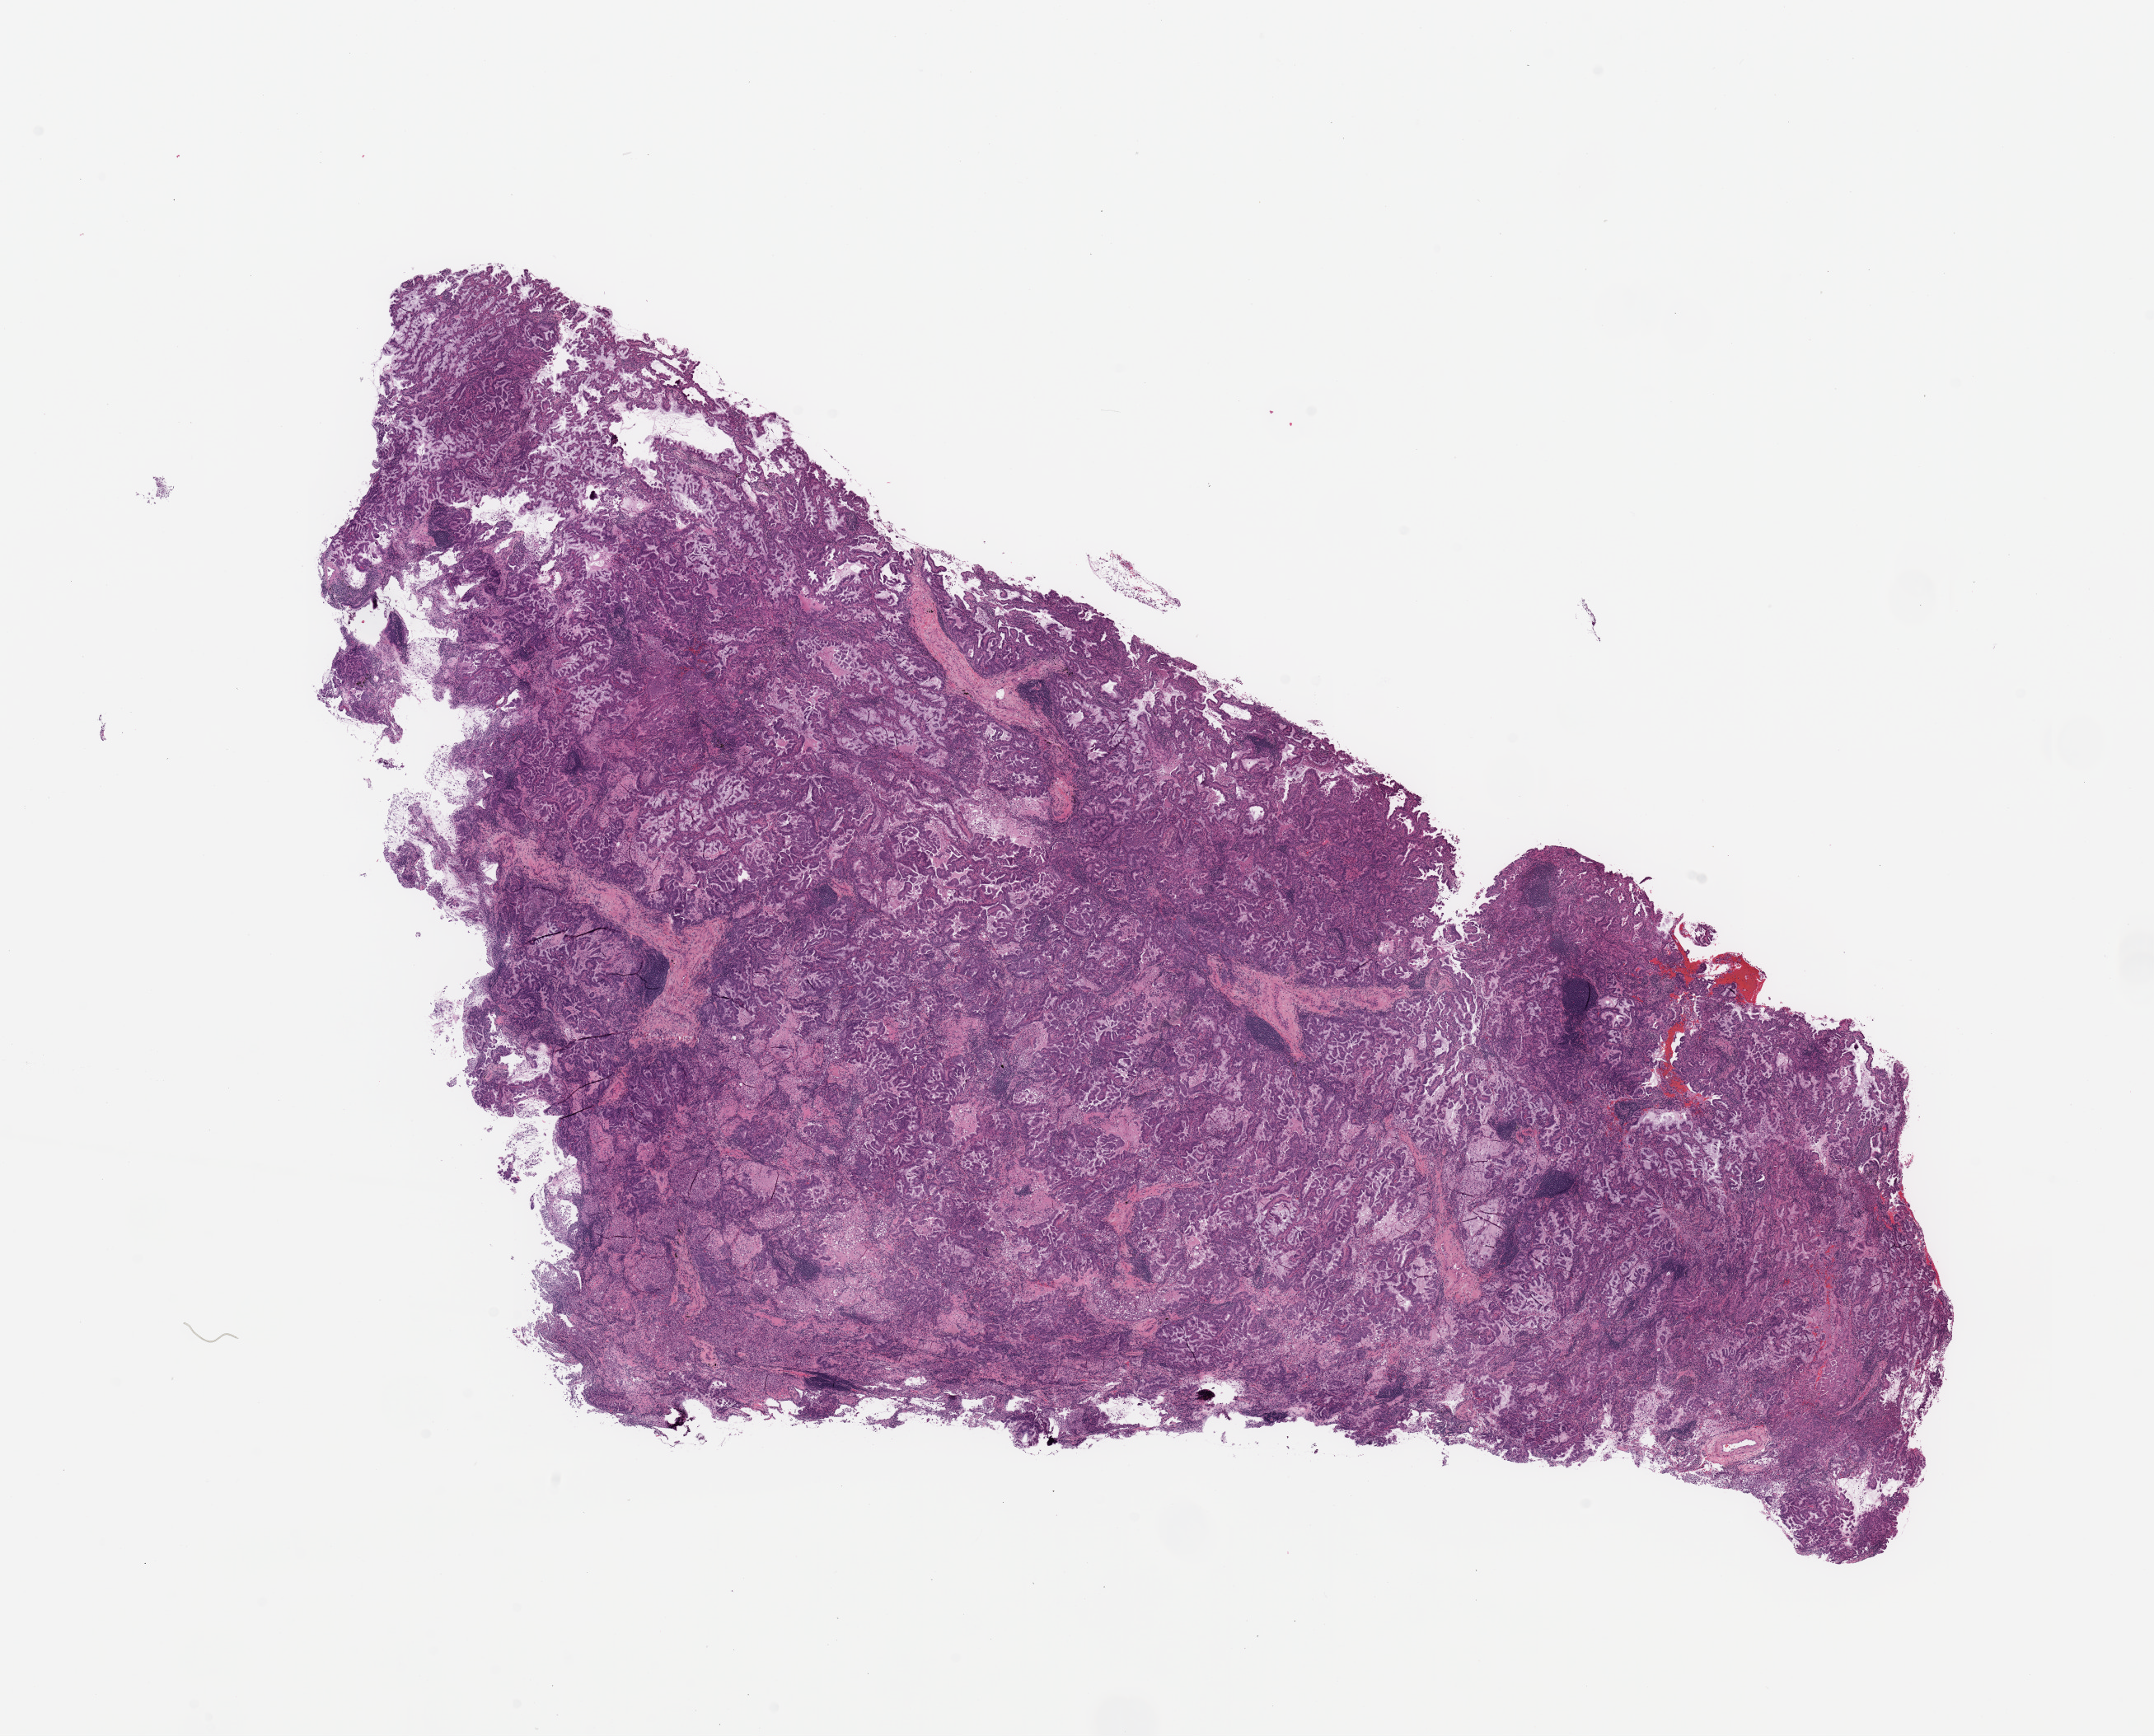
H&E-stained whole-slide image, low-resolution overview of the scanned area, about 20.7 x 16.7 mm (from a 20x scan), lung, tumour tissue. Male, 76 y/o. Histologic grade: G2 (moderately differentiated).
* AJCC pathologic stage: IB
* primary tumour site (as recorded): right lower lobe
* histologic diagnosis: Adenocarcinoma, NOS